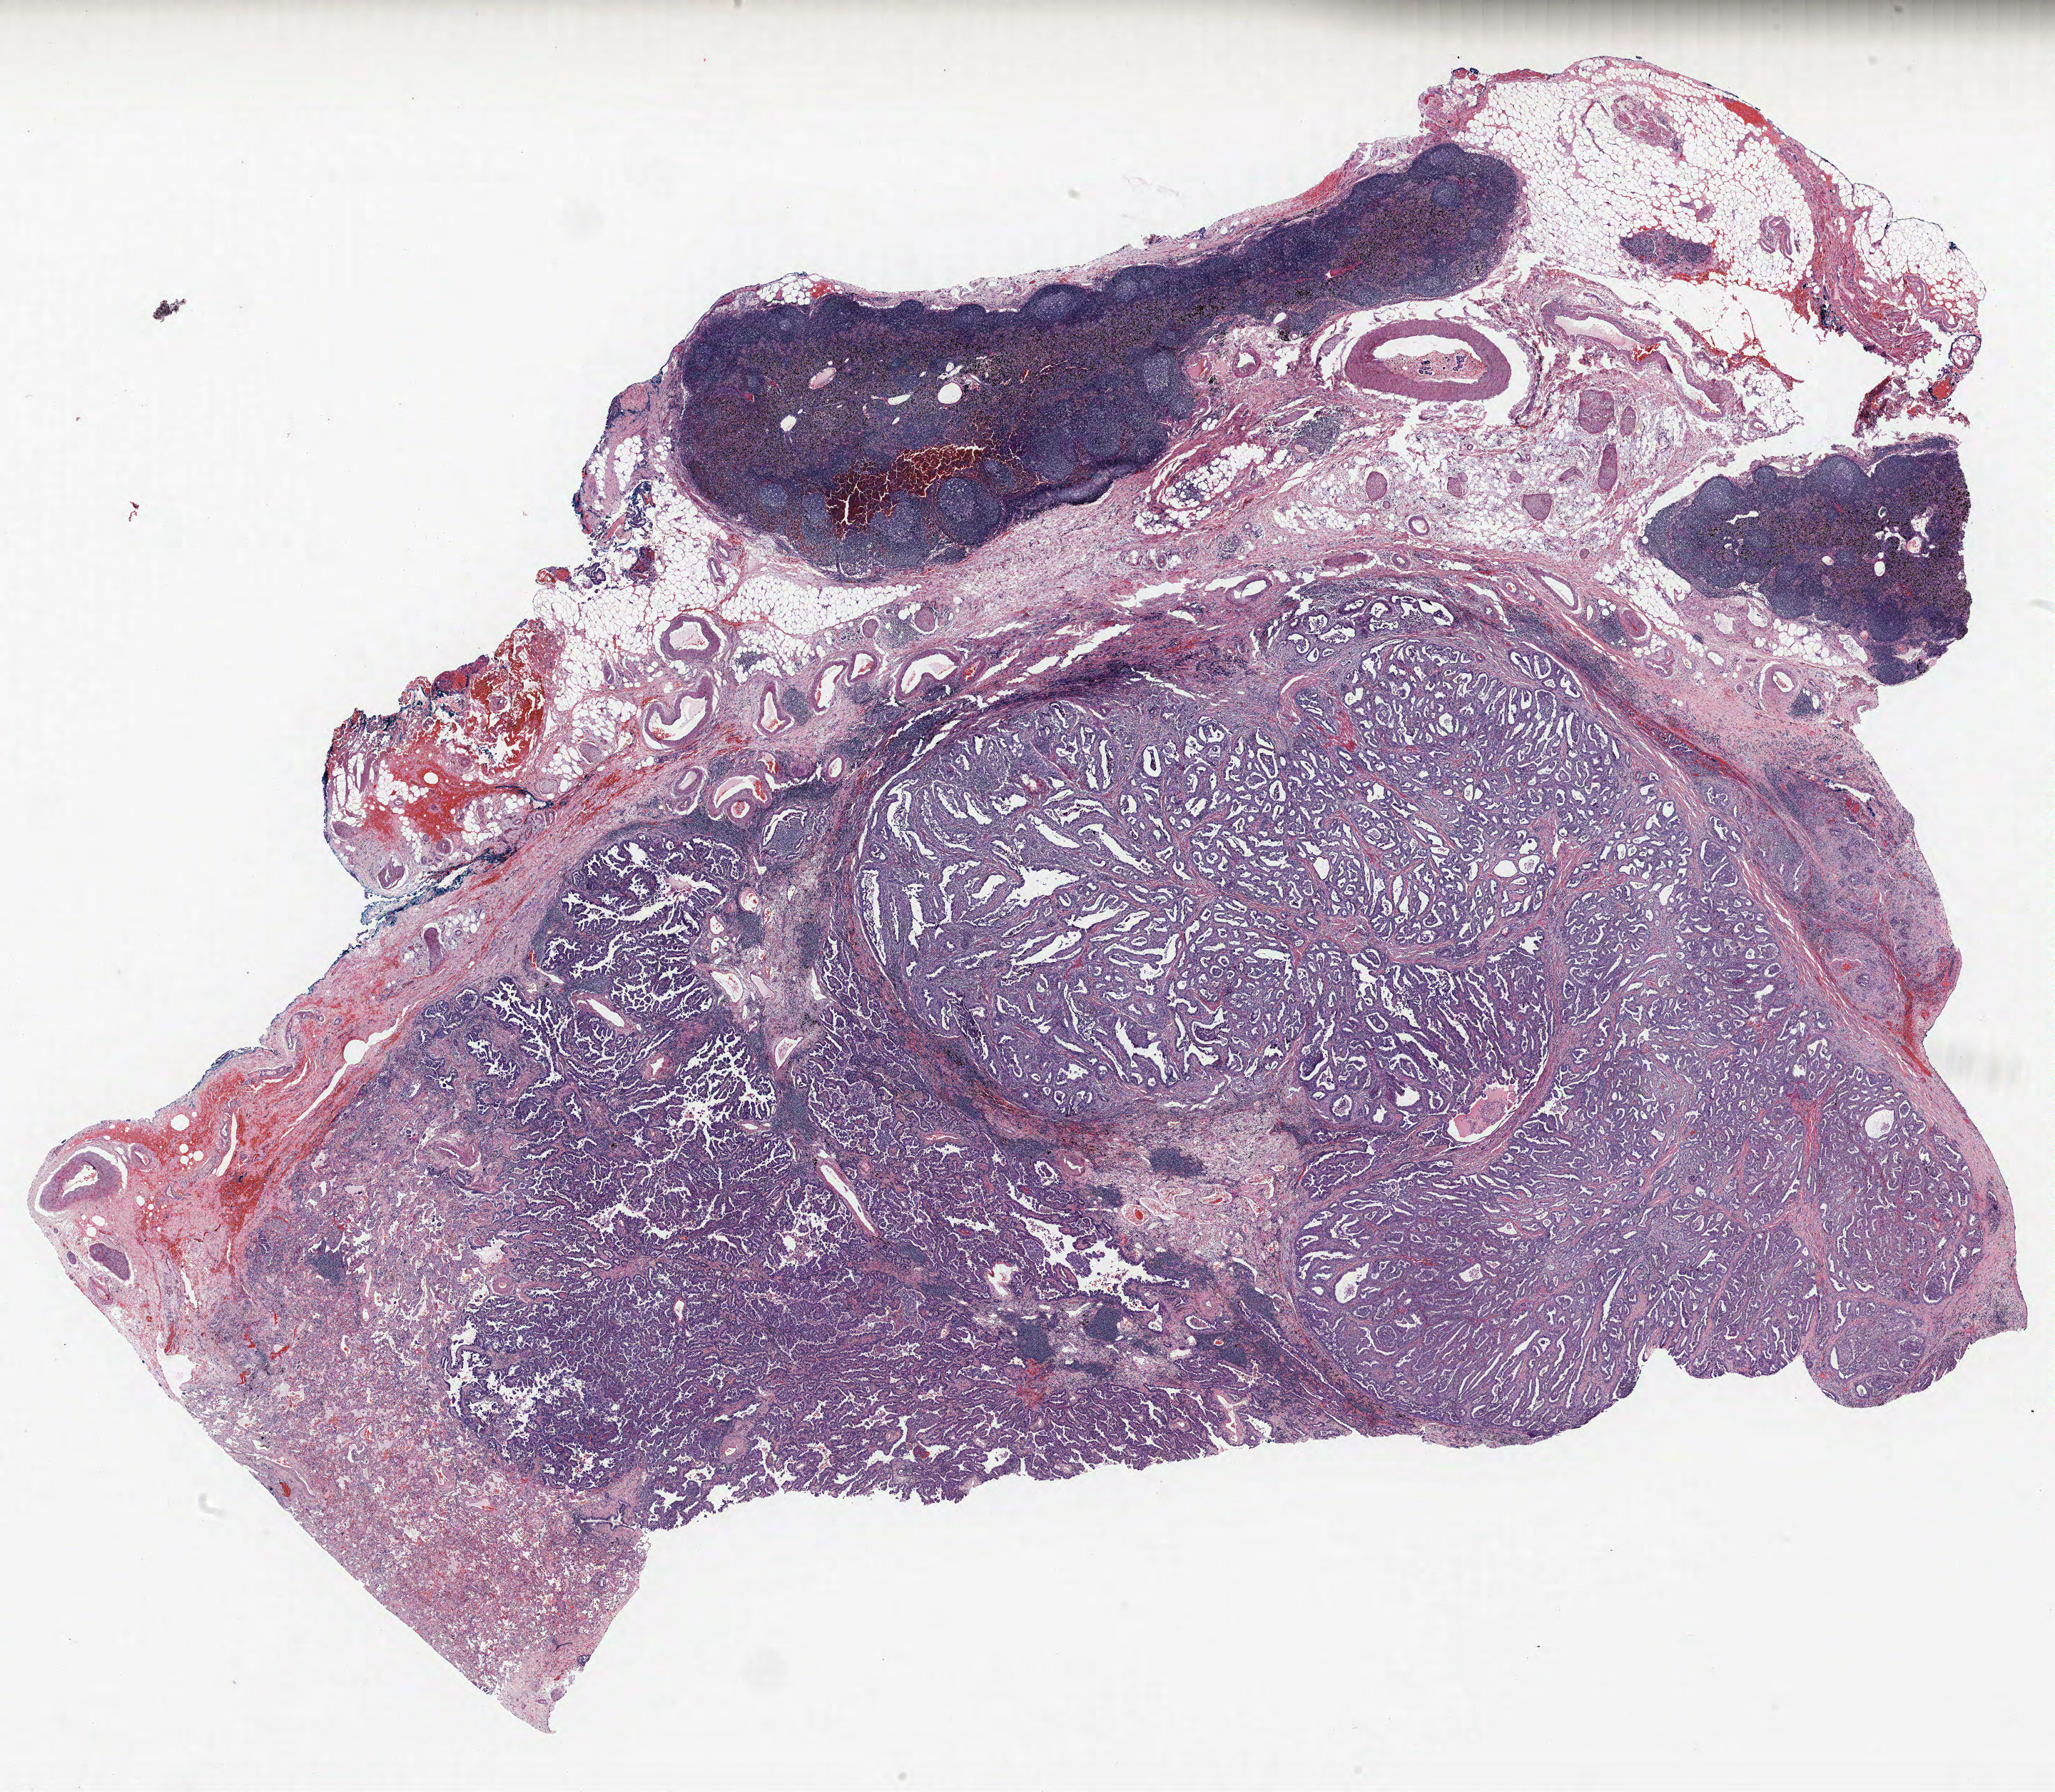
Whole-slide histology image, H&E, a low-resolution overview of the entire scanned area, about 23.0 x 20.1 mm (acquisition: 40x scan), formalin-fixed paraffin-embedded (FFPE) section, lung tissue. Female patient, aged 68 at enrolment. Former smoker at enrolment. Grade: moderately differentiated (G2).
• stage (AJCC 6th edition): IB
• participant's lung-cancer diagnosis: Adenocarcinoma, NOS
• primary tumour location (clinical record): right lower lobe
• tumour size (pathology): 40 mm